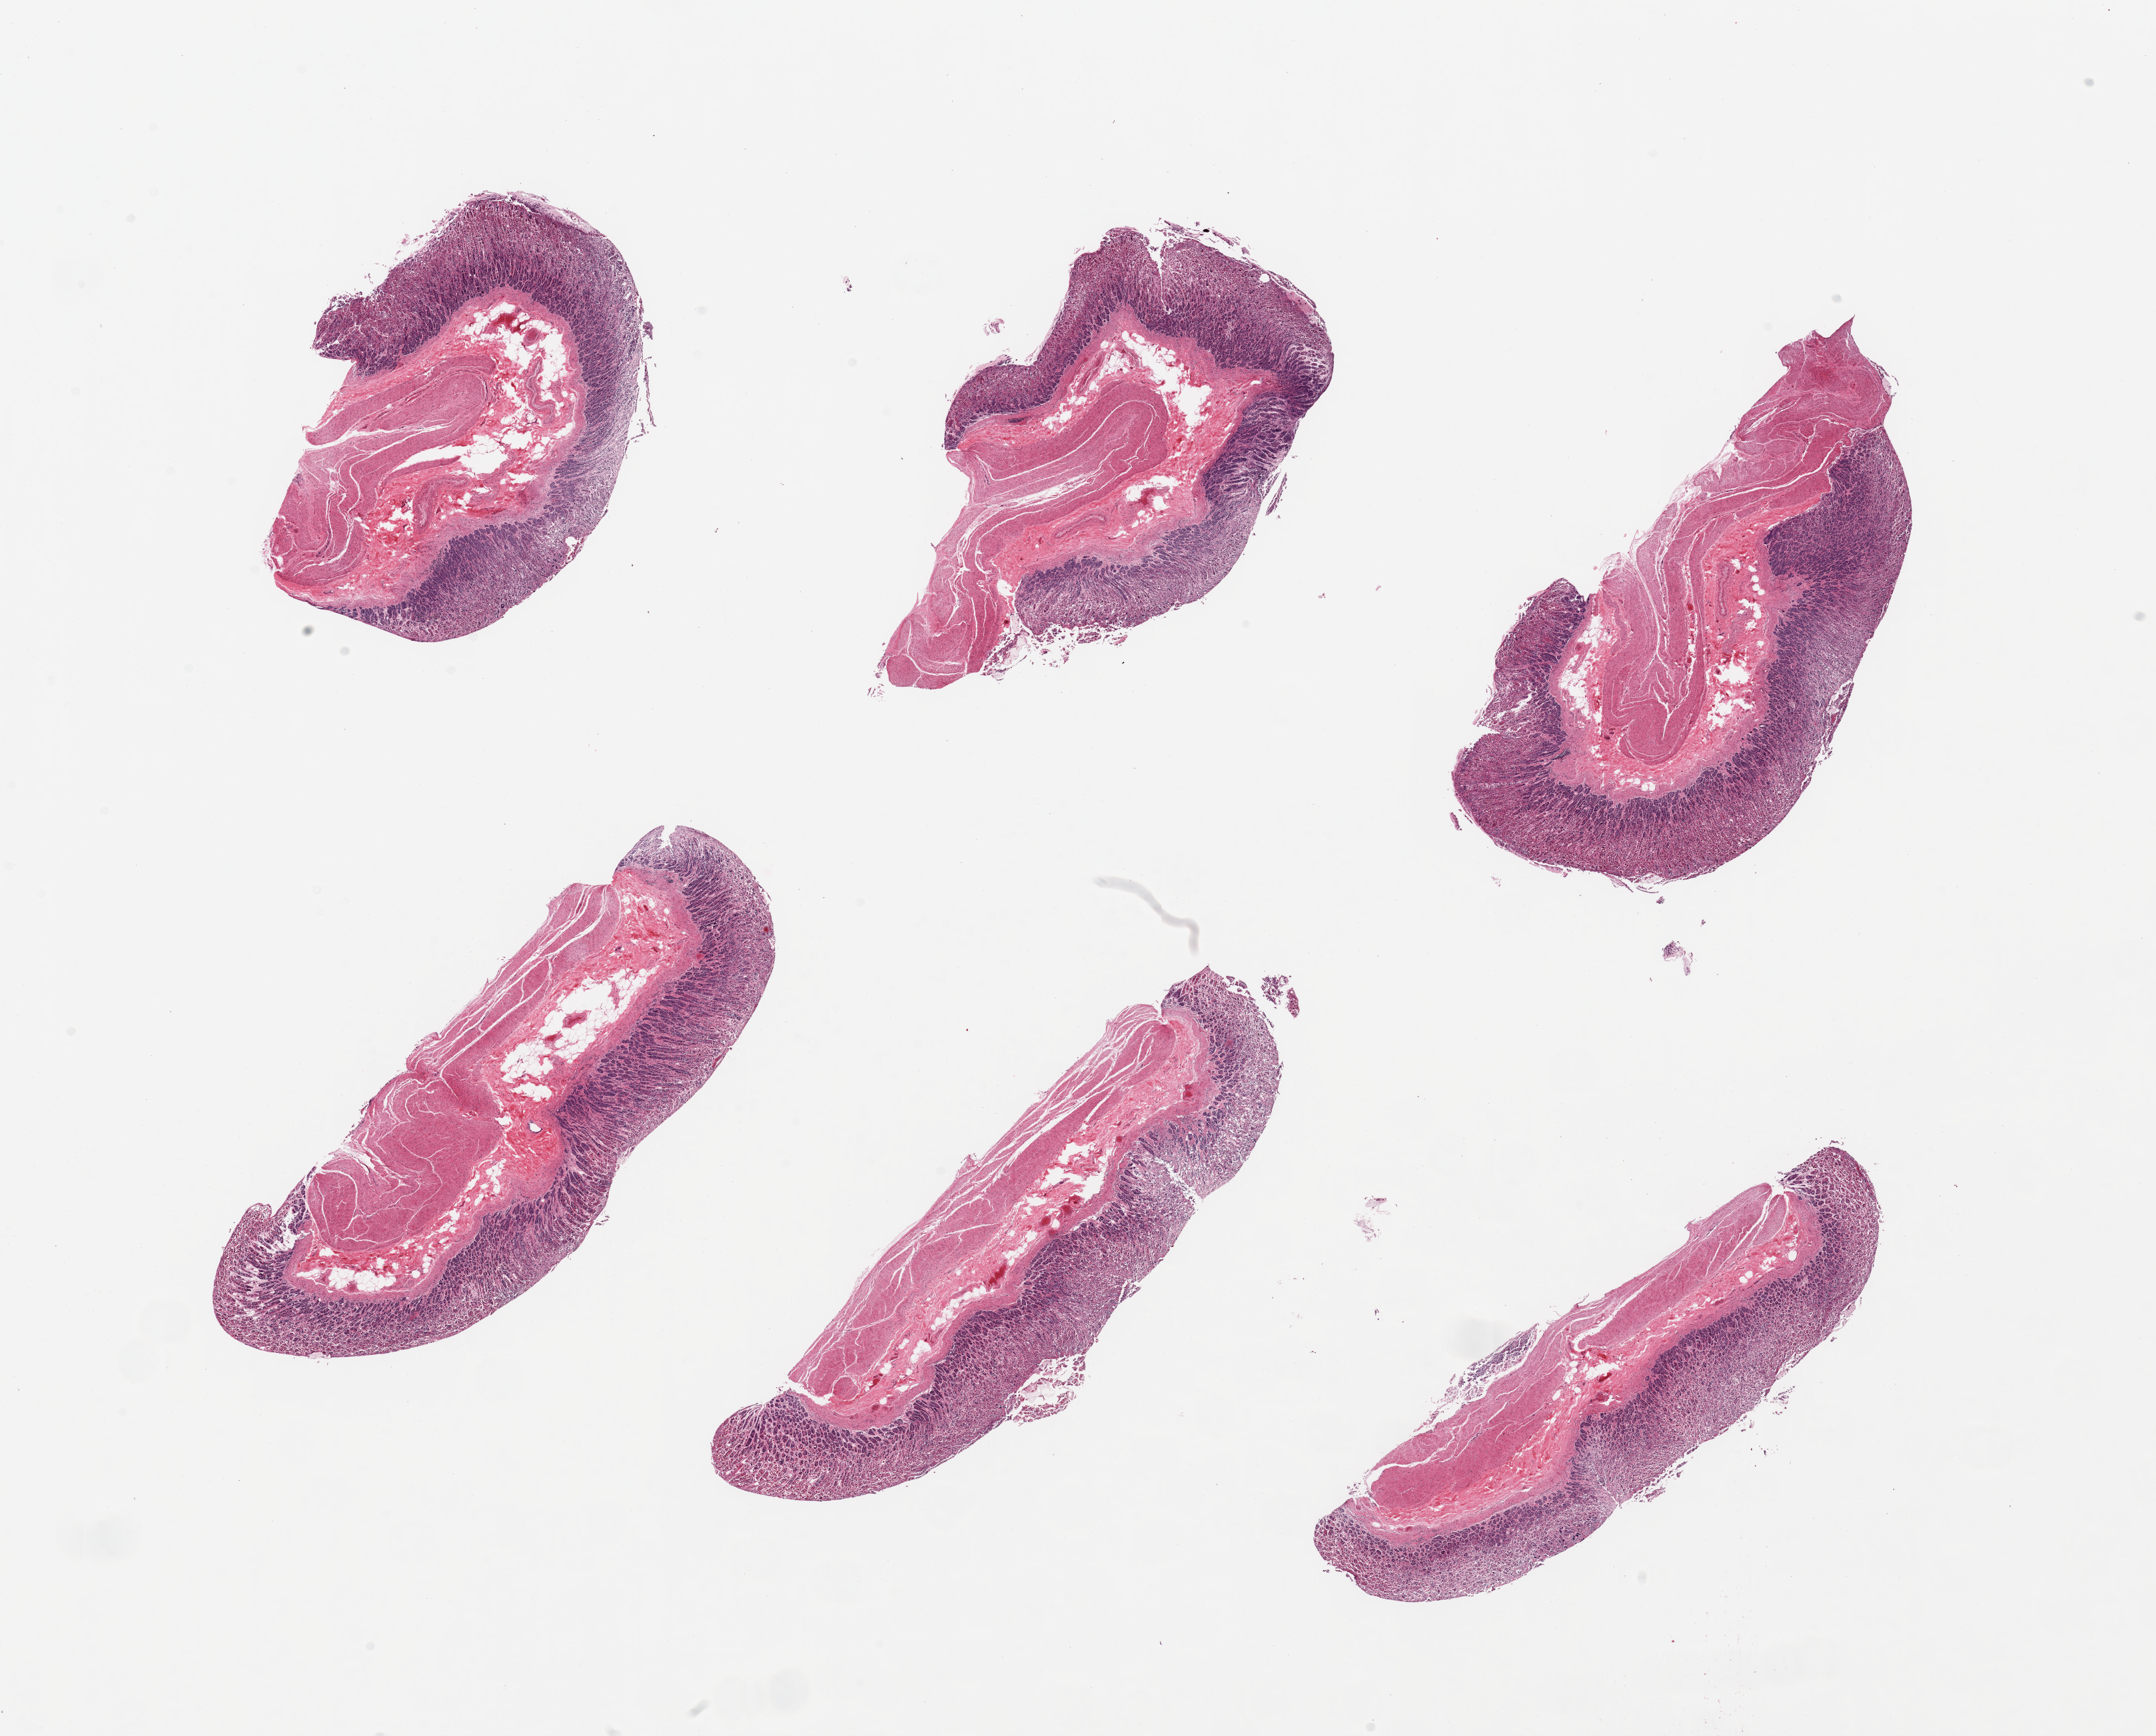
Whole-slide image, hematoxylin and eosin (H&E) stain, brightfield — whole scanned area (about 25.6 x 20.6 mm) shown as a low-resolution overview, PAXgene-fixed paraffin-embedded (PFPE) section, target tissue: stomach, donor tissue sample.
Reviewer comment on this tissue sample: 6 pieces, moderately autolyzed mucosa and musculairs.